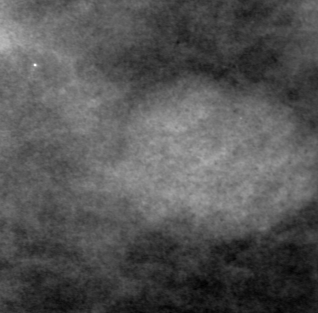
Cropped region of a digitized screen-film mammogram centred on a radiologist-marked abnormality, right breast, CC view.
Finding: mass, shape oval, margins circumscribed; BI-RADS assessment category 0 (incomplete: needs additional imaging); pathology result (as recorded, not read from the image): benign.